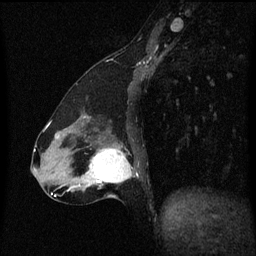
Breast MRI (dynamic contrast-enhanced), one sagittal slice. Slice 22 of 60 in the series (ordered by position). Dynamic contrast-enhanced series, image 2 of 3 at this slice position (ordered by acquisition). 1.5 T. TE 4.2 ms, TR 8.4 ms. 2 mm slice thickness. 256 × 256 image matrix. Female patient, age 47 years.
Annotated regions visible in this slice (semi-automatically segmented with operator editing):
- analysis volume of interest (the breast-tissue region the enhancement analysis was run in; not a lesion): box from (x=81, y=140) to (x=135, y=197) px
- tumour enhancement mask (voxels above the 70 % enhancement threshold inside the analysis volume of interest): (x=89, y=148)–(x=132, y=183)